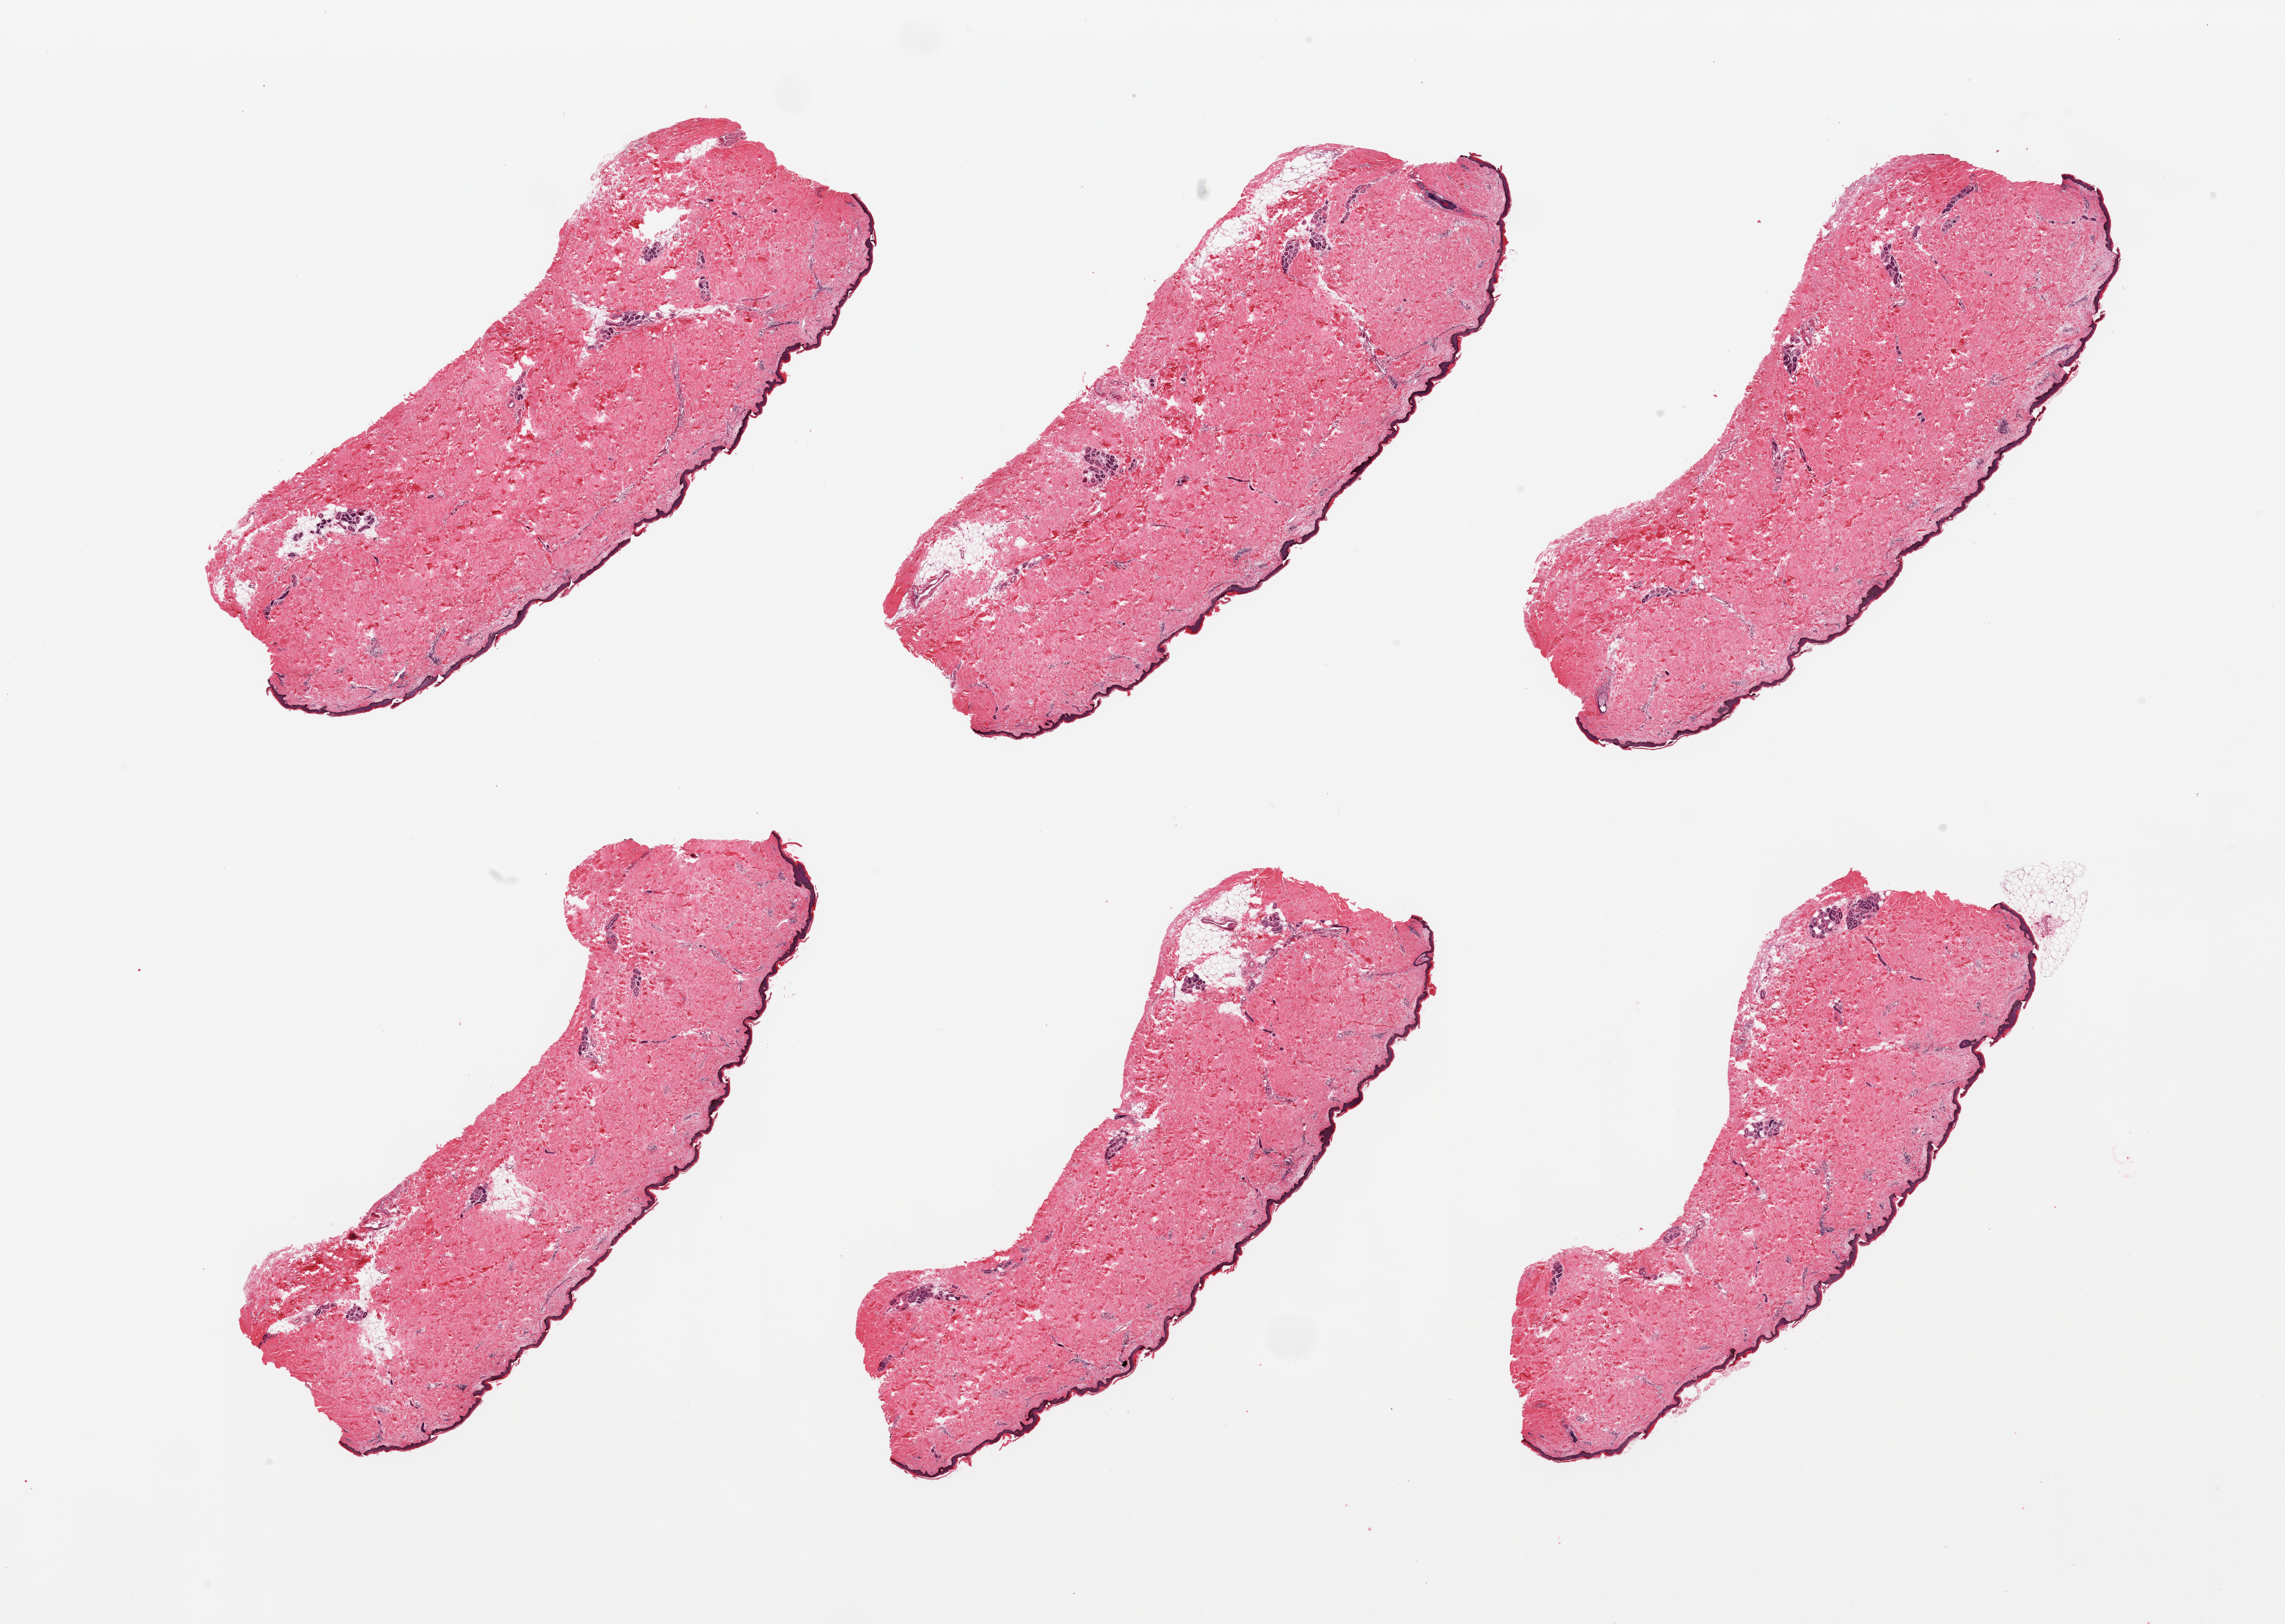
Whole-slide image, haematoxylin and eosin stain — shown as a low-resolution overview of the whole scanned area (about 29.5 x 21.0 mm, slide scanned at 20x). PAXgene-fixed paraffin-embedded (PFPE) section. Target tissue: skin of lower leg. Donor tissue sample. Male donor.
Reviewer comment on this tissue sample: 6 pieces, squamous epithelium is ~50 microns; minimal adherent dermal fat.